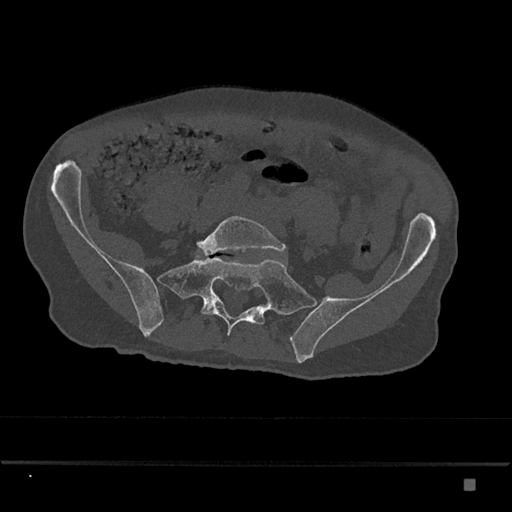
CT including the spine, one axial slice. 120 kVp. Bone window (W 1800 / L 400 HU). 512 × 512 image matrix, field of view 390 × 390 mm. Patient: male, 72 years. Case-level facts recorded for this patient, not image findings: primary cancer: prostate.
Structures marked on this image (semi-automatically segmented with operator editing):
- L5 vertebra: bounding box (x1, y1, x2, y2) in pixels: (197, 216, 287, 256)